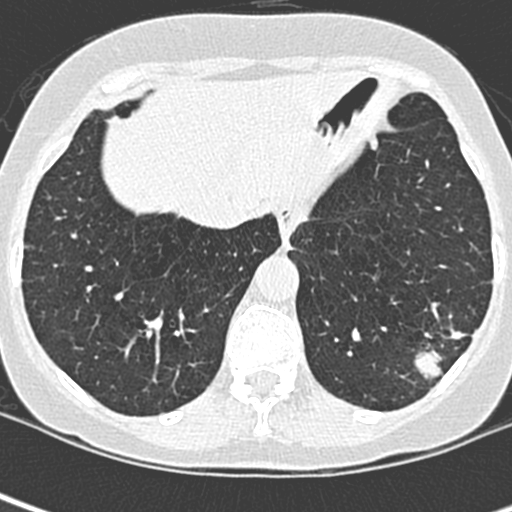
Low-dose screening chest CT, one axial slice; slice 69 of 252 in the series (ordered by position); lung window (W 1500 / L -600 HU); 1.3 mm slice thickness; 512 × 512 image matrix, field of view 271 × 271 mm.
Outlined on this slice (manually delineated by an expert):
- lesion 1 (tumor, lower lobe of left lung): box from (x=414, y=326) to (x=465, y=380) px